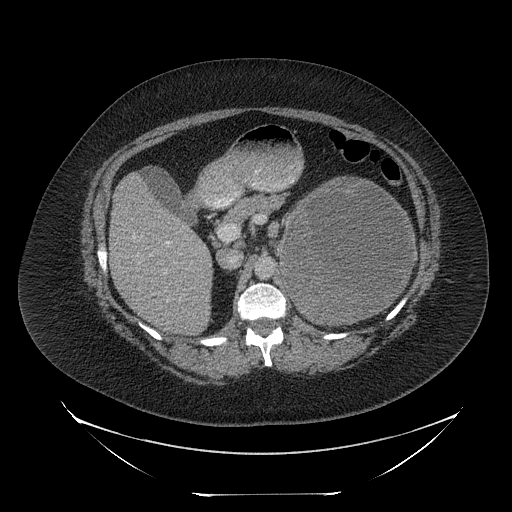
Contrast-enhanced abdominal CT, one axial slice. Position 142 of 205 along the scan axis. Reconstruction kernel STANDARD. 120 kVp. Intravenous contrast given. Soft-tissue window (W 400 / L 40 HU). 2.5 mm slice thickness. 512 × 512 image matrix, field of view 500 × 500 mm. Female patient, age 53 years. From the clinical record (not read from this slice): diagnosis: adrenocortical carcinoma; tumour side: left adrenal; tumour size at pathology: 17 cm; Ki-67 index: 20 %; stage (as recorded): 3.
Annotated regions visible in this slice (semi-automatically segmented with operator editing):
- mass: box from (x=281, y=179) to (x=412, y=320) px